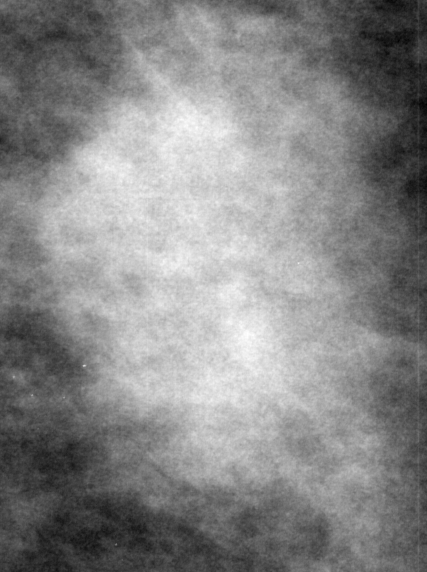
Region of interest cut from a scanned film mammogram (one marked finding); right breast; CC view; BI-RADS breast density category 3 (scale 1–4).
- Marked abnormality: mass, shape irregular, margins ill defined; BI-RADS assessment category 4; pathology (as recorded): malignant.